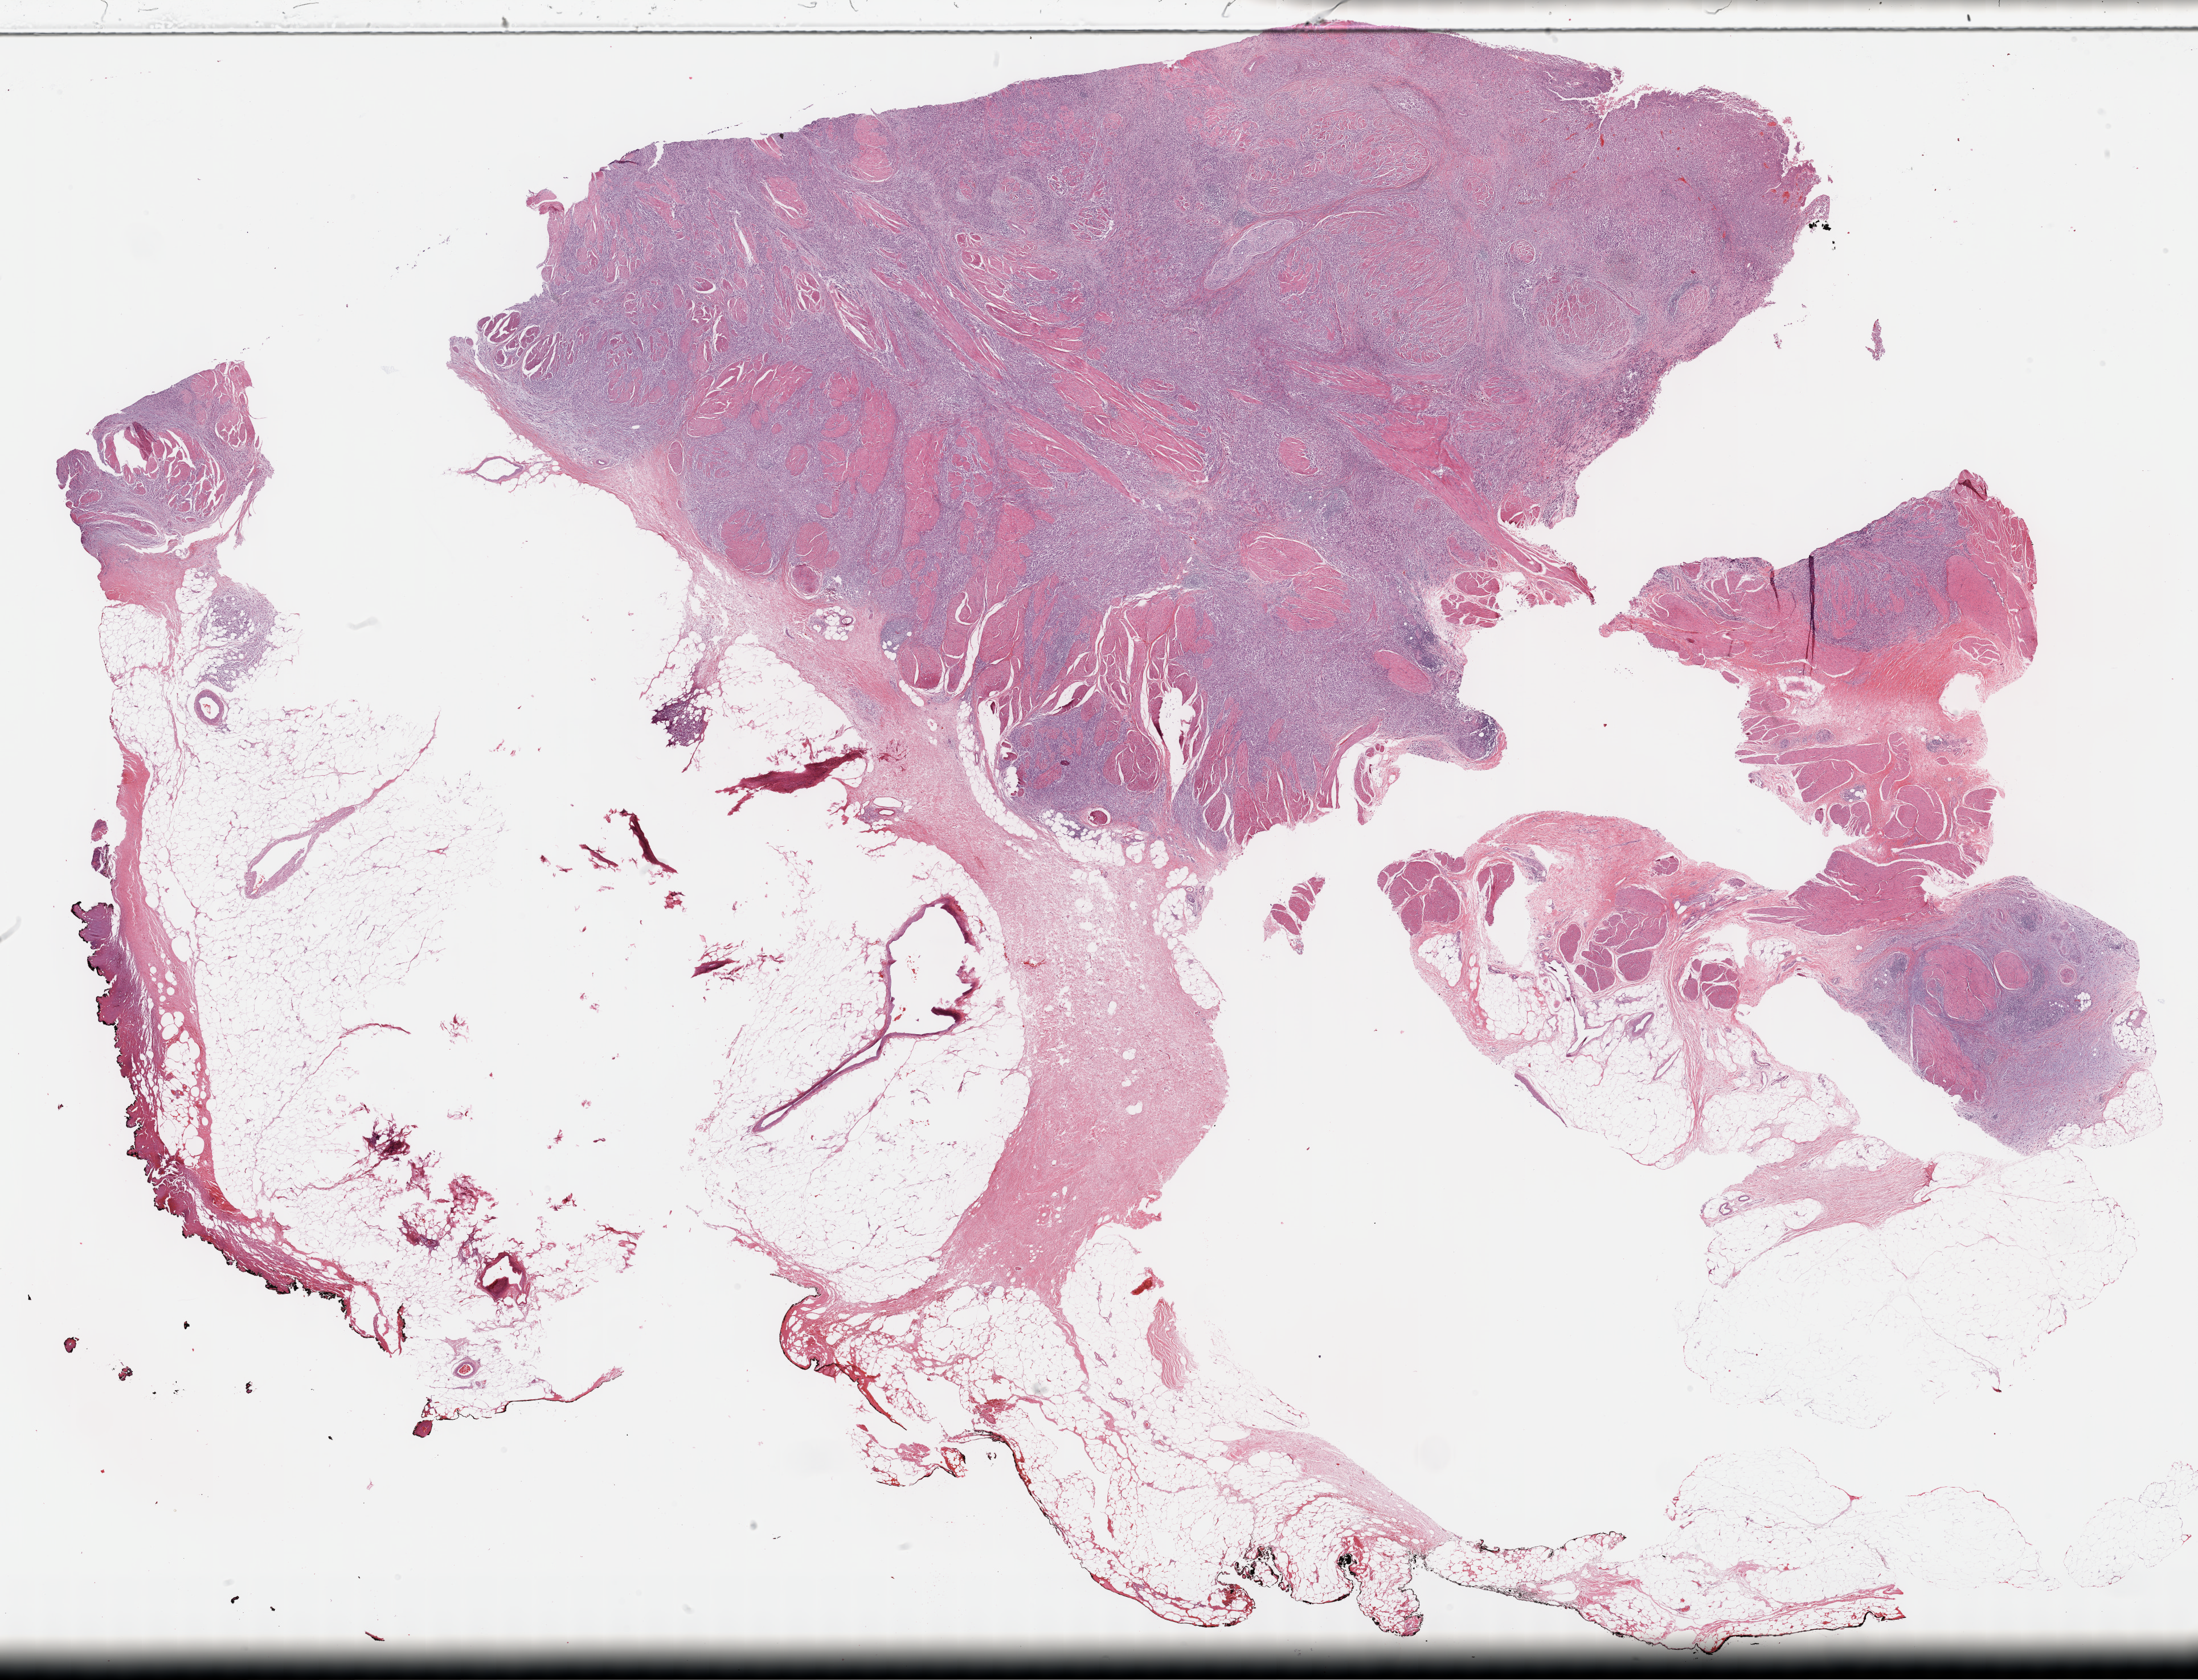
Whole-slide histology image, H&E — whole scanned area (about 31.2 x 23.9 mm) shown as a low-resolution overview, FFPE section, sample: primary tumour, bladder. Male, age 68 years at initial diagnosis. Histologic grade: high grade.
Histologic diagnosis: Transitional cell carcinoma. Lymph nodes positive (case pathology): 30 of 53 examined. AJCC pathologic stage: IV.